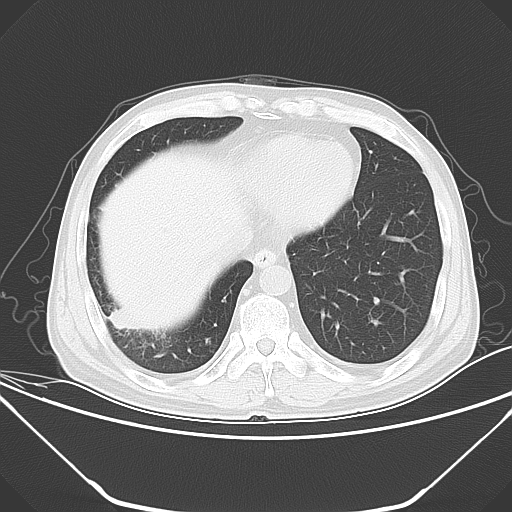
Chest CT, one axial slice; position 12 of 52 along the scan axis; lung window (W 1500 / L -600 HU); 5 mm slice thickness; 512 × 512 image matrix, field of view 379 × 379 mm. Male patient, age 54 years. Case-level facts recorded for this patient, not image findings: clinical TNM (as recorded): T2 N1 M0.
Annotated regions visible in this slice (bounding box drawn by a radiologist):
- lung tumour (recorded histology: adenocarcinoma): bounding box (x1, y1, x2, y2) in pixels: (108, 304, 135, 327)